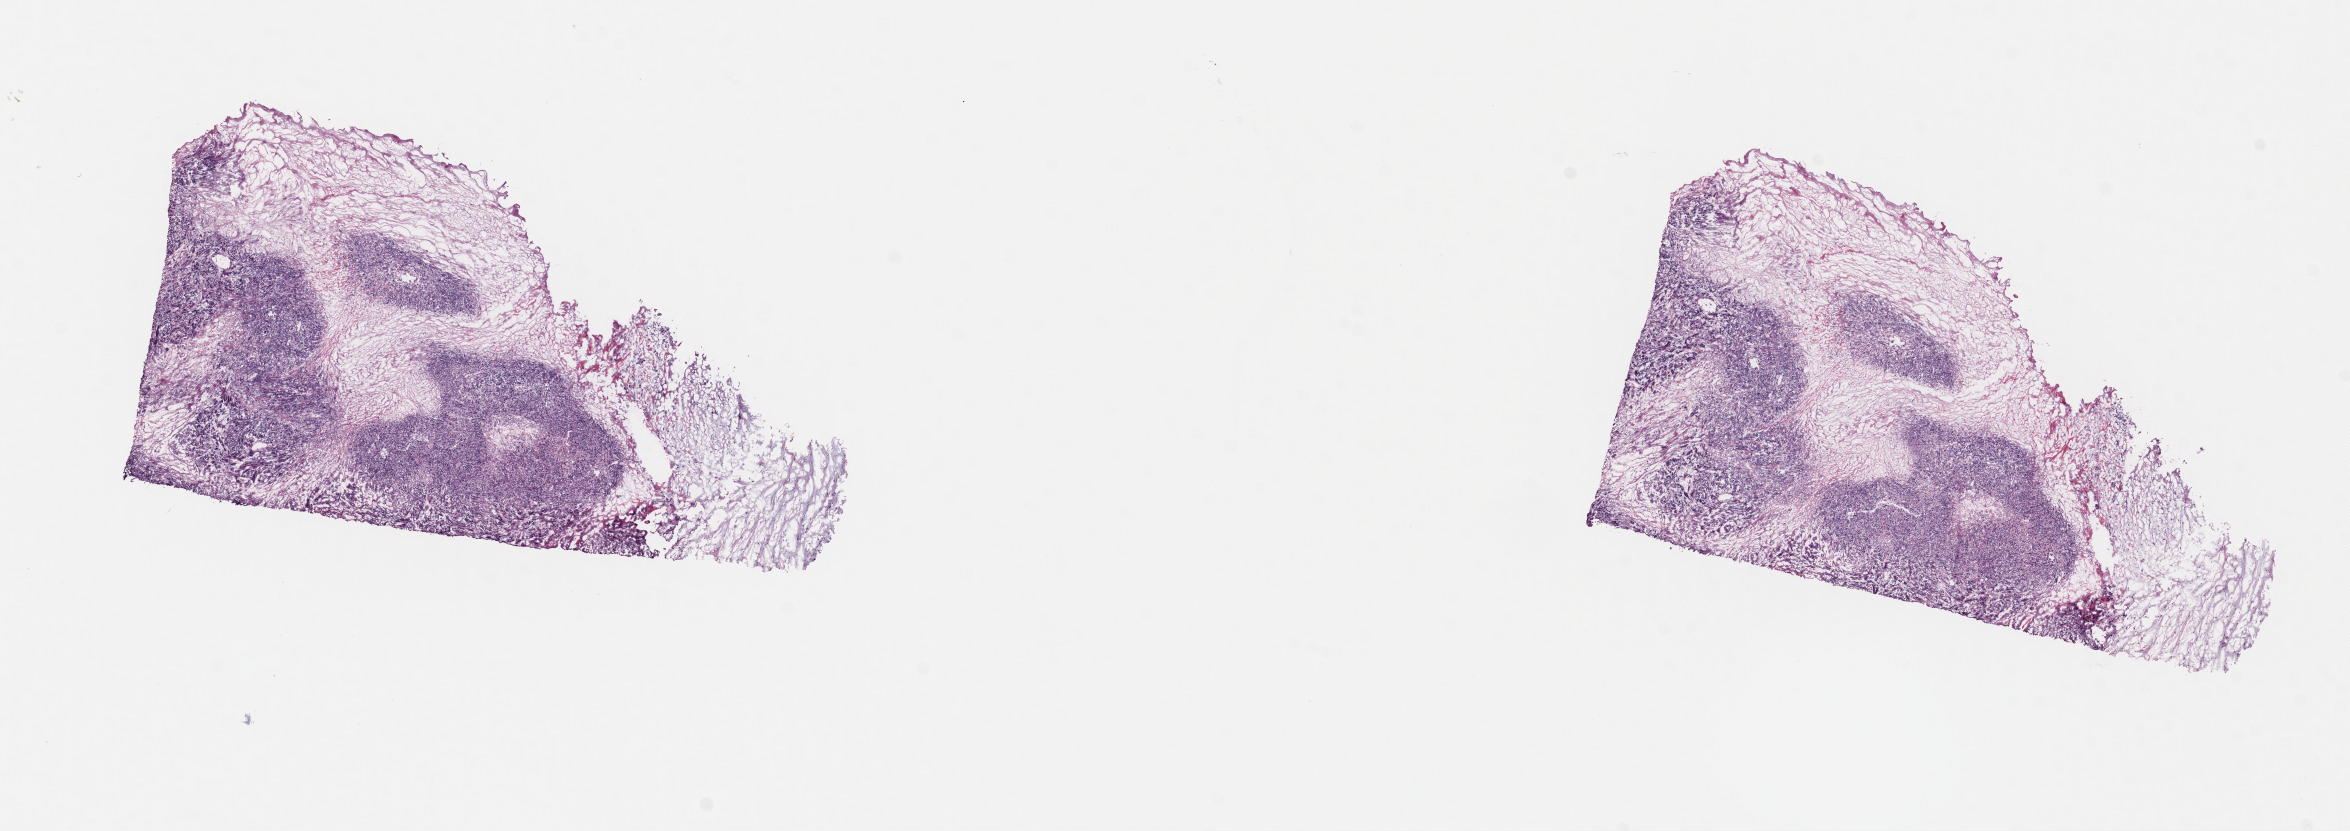
Whole-slide histology image, H&E-stained — low-resolution overview of the scanned area, about 18.5 x 6.5 mm, frozen section from the top of the tissue portion, metastatic tumour sample. Male, age 43 years at initial diagnosis. Composition of this section per pathologist review: tumour cells 60%, tumour nuclei 85%, normal cells 0%, stromal cells 40%, necrosis 0%. Infiltration values recorded for this section: lymphocyte infiltration 0%, monocyte infiltration 0%, neutrophil infiltration 0%.
This section: metastatic tumour tissue. Patient diagnosis: Malignant melanoma, NOS.